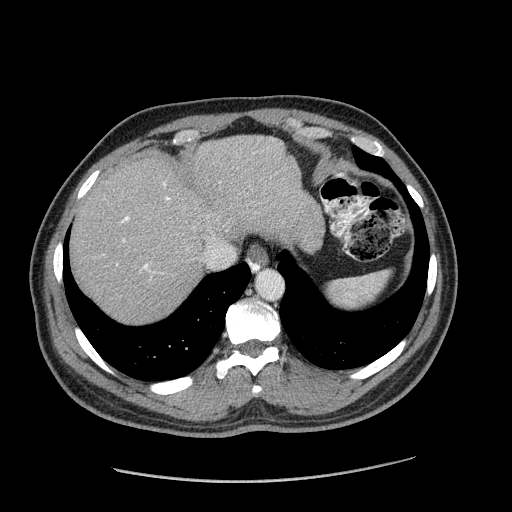
Contrast-enhanced abdominal CT (liver protocol), one axial slice. Position 149 of 182 along the scan axis. Soft-tissue window (W 400 / L 40 HU). 2.5 mm slice thickness. 512 × 512 image matrix. Case-level facts recorded for this patient, not image findings: diagnosis: hepatocellular carcinoma (patient treated with transarterial chemoembolisation; whether this scan precedes or follows treatment is not stated here); TNM stage (as recorded): Stage-I; Child-Pugh class: A; tumour differentiation: well differentiated; tumour nodularity: uninodular.
Annotated regions visible in this slice (semi-automatically segmented with operator editing):
- abdominal aorta: bounding box (x1, y1, x2, y2) in pixels: (258, 272, 283, 299)
- liver parenchyma outside the tumour (the mass and vessels are separate outlines, so this box may not span the whole liver): (70, 134, 324, 322)
- liver vessels: (122, 183, 170, 269)